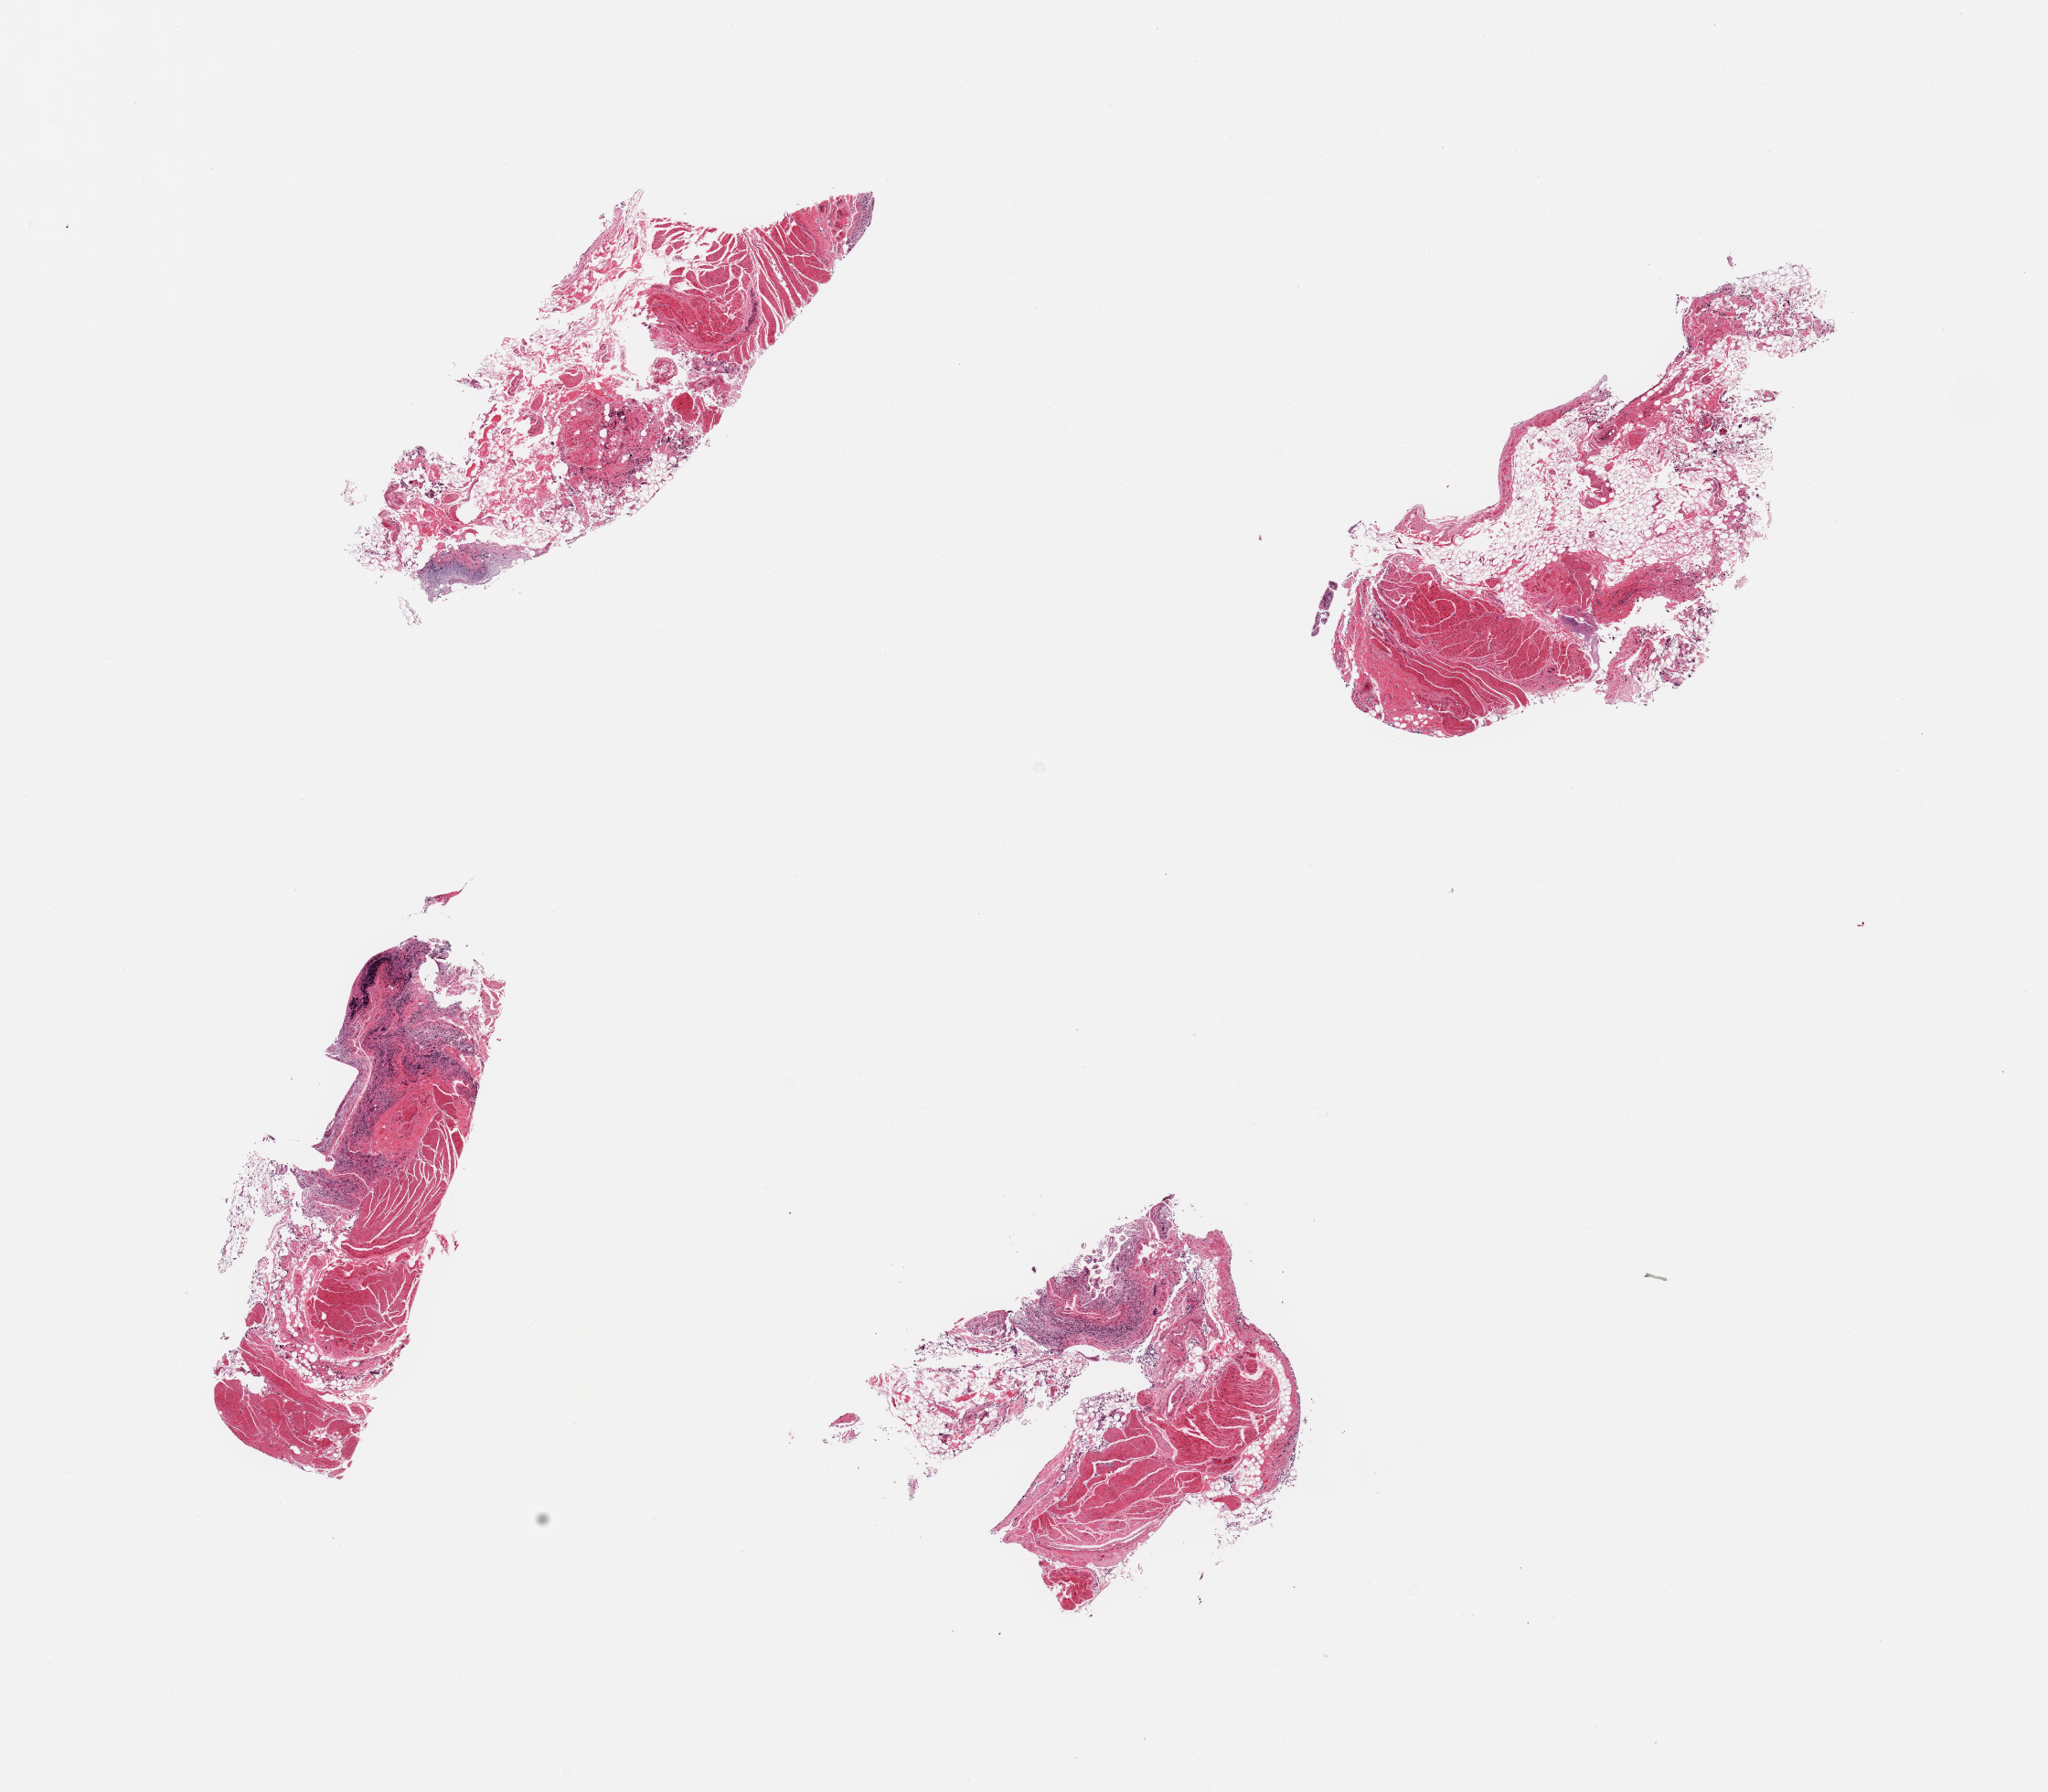
Whole-slide image, hematoxylin and eosin (H&E) stain, low-resolution overview of the scanned area, about 17.7 x 15.5 mm, PAXgene-fixed paraffin-embedded (PFPE) section, sampled site (target tissue): ileum, tissue donor sample. Donor sex: female.
Pathologist's review note for this sample: 4 pieces; no evidence of viable mucosa and no lymphoid nodules.